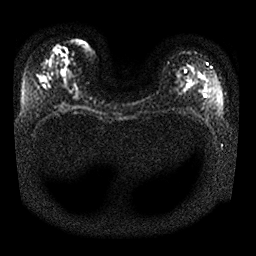
Breast MRI, one axial slice. Position 15 of 25 along the scan axis. Diffusion-weighted series; image 2 of 4 stored at this slice position (different b-values; order by instance number). 1.5 T. 4 mm slice thickness. 256 × 256 image matrix, field of view 340 × 340 mm. Female patient.
Outlined on this slice (outlined manually by an expert reader):
- tumour on diffusion-weighted imaging: bounding box [x1, y1, x2, y2] px = [52, 44, 68, 57]